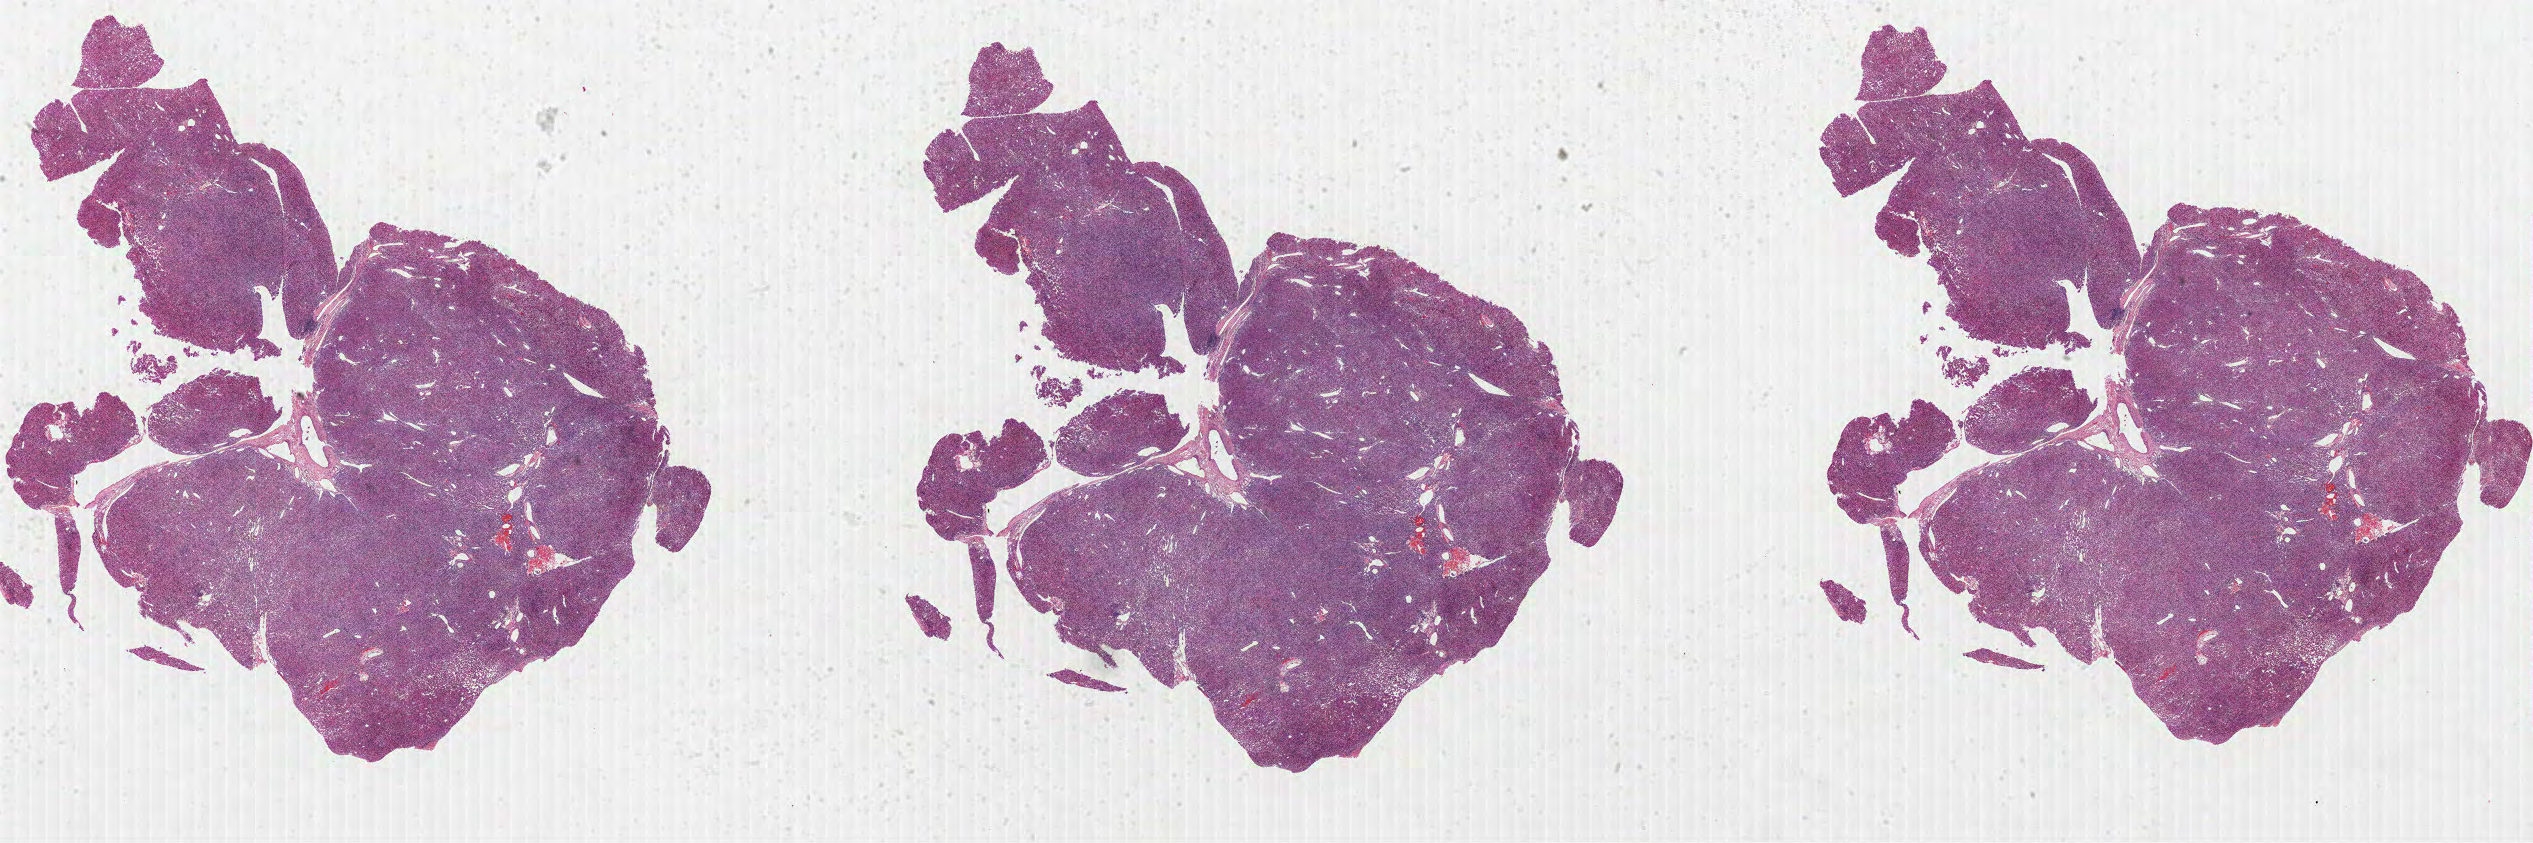
Whole-slide histology image, H&E — shown as a low-resolution overview of the whole scanned area (about 40.9 x 13.6 mm). FFPE section. Sample: primary tumour, kidney. Patient: female, age at initial diagnosis 63 years. Histologic grade: G3 (poorly differentiated).
• AJCC pathologic stage: I (6th edition)
• laterality: left
• diagnosis: Clear cell adenocarcinoma, NOS